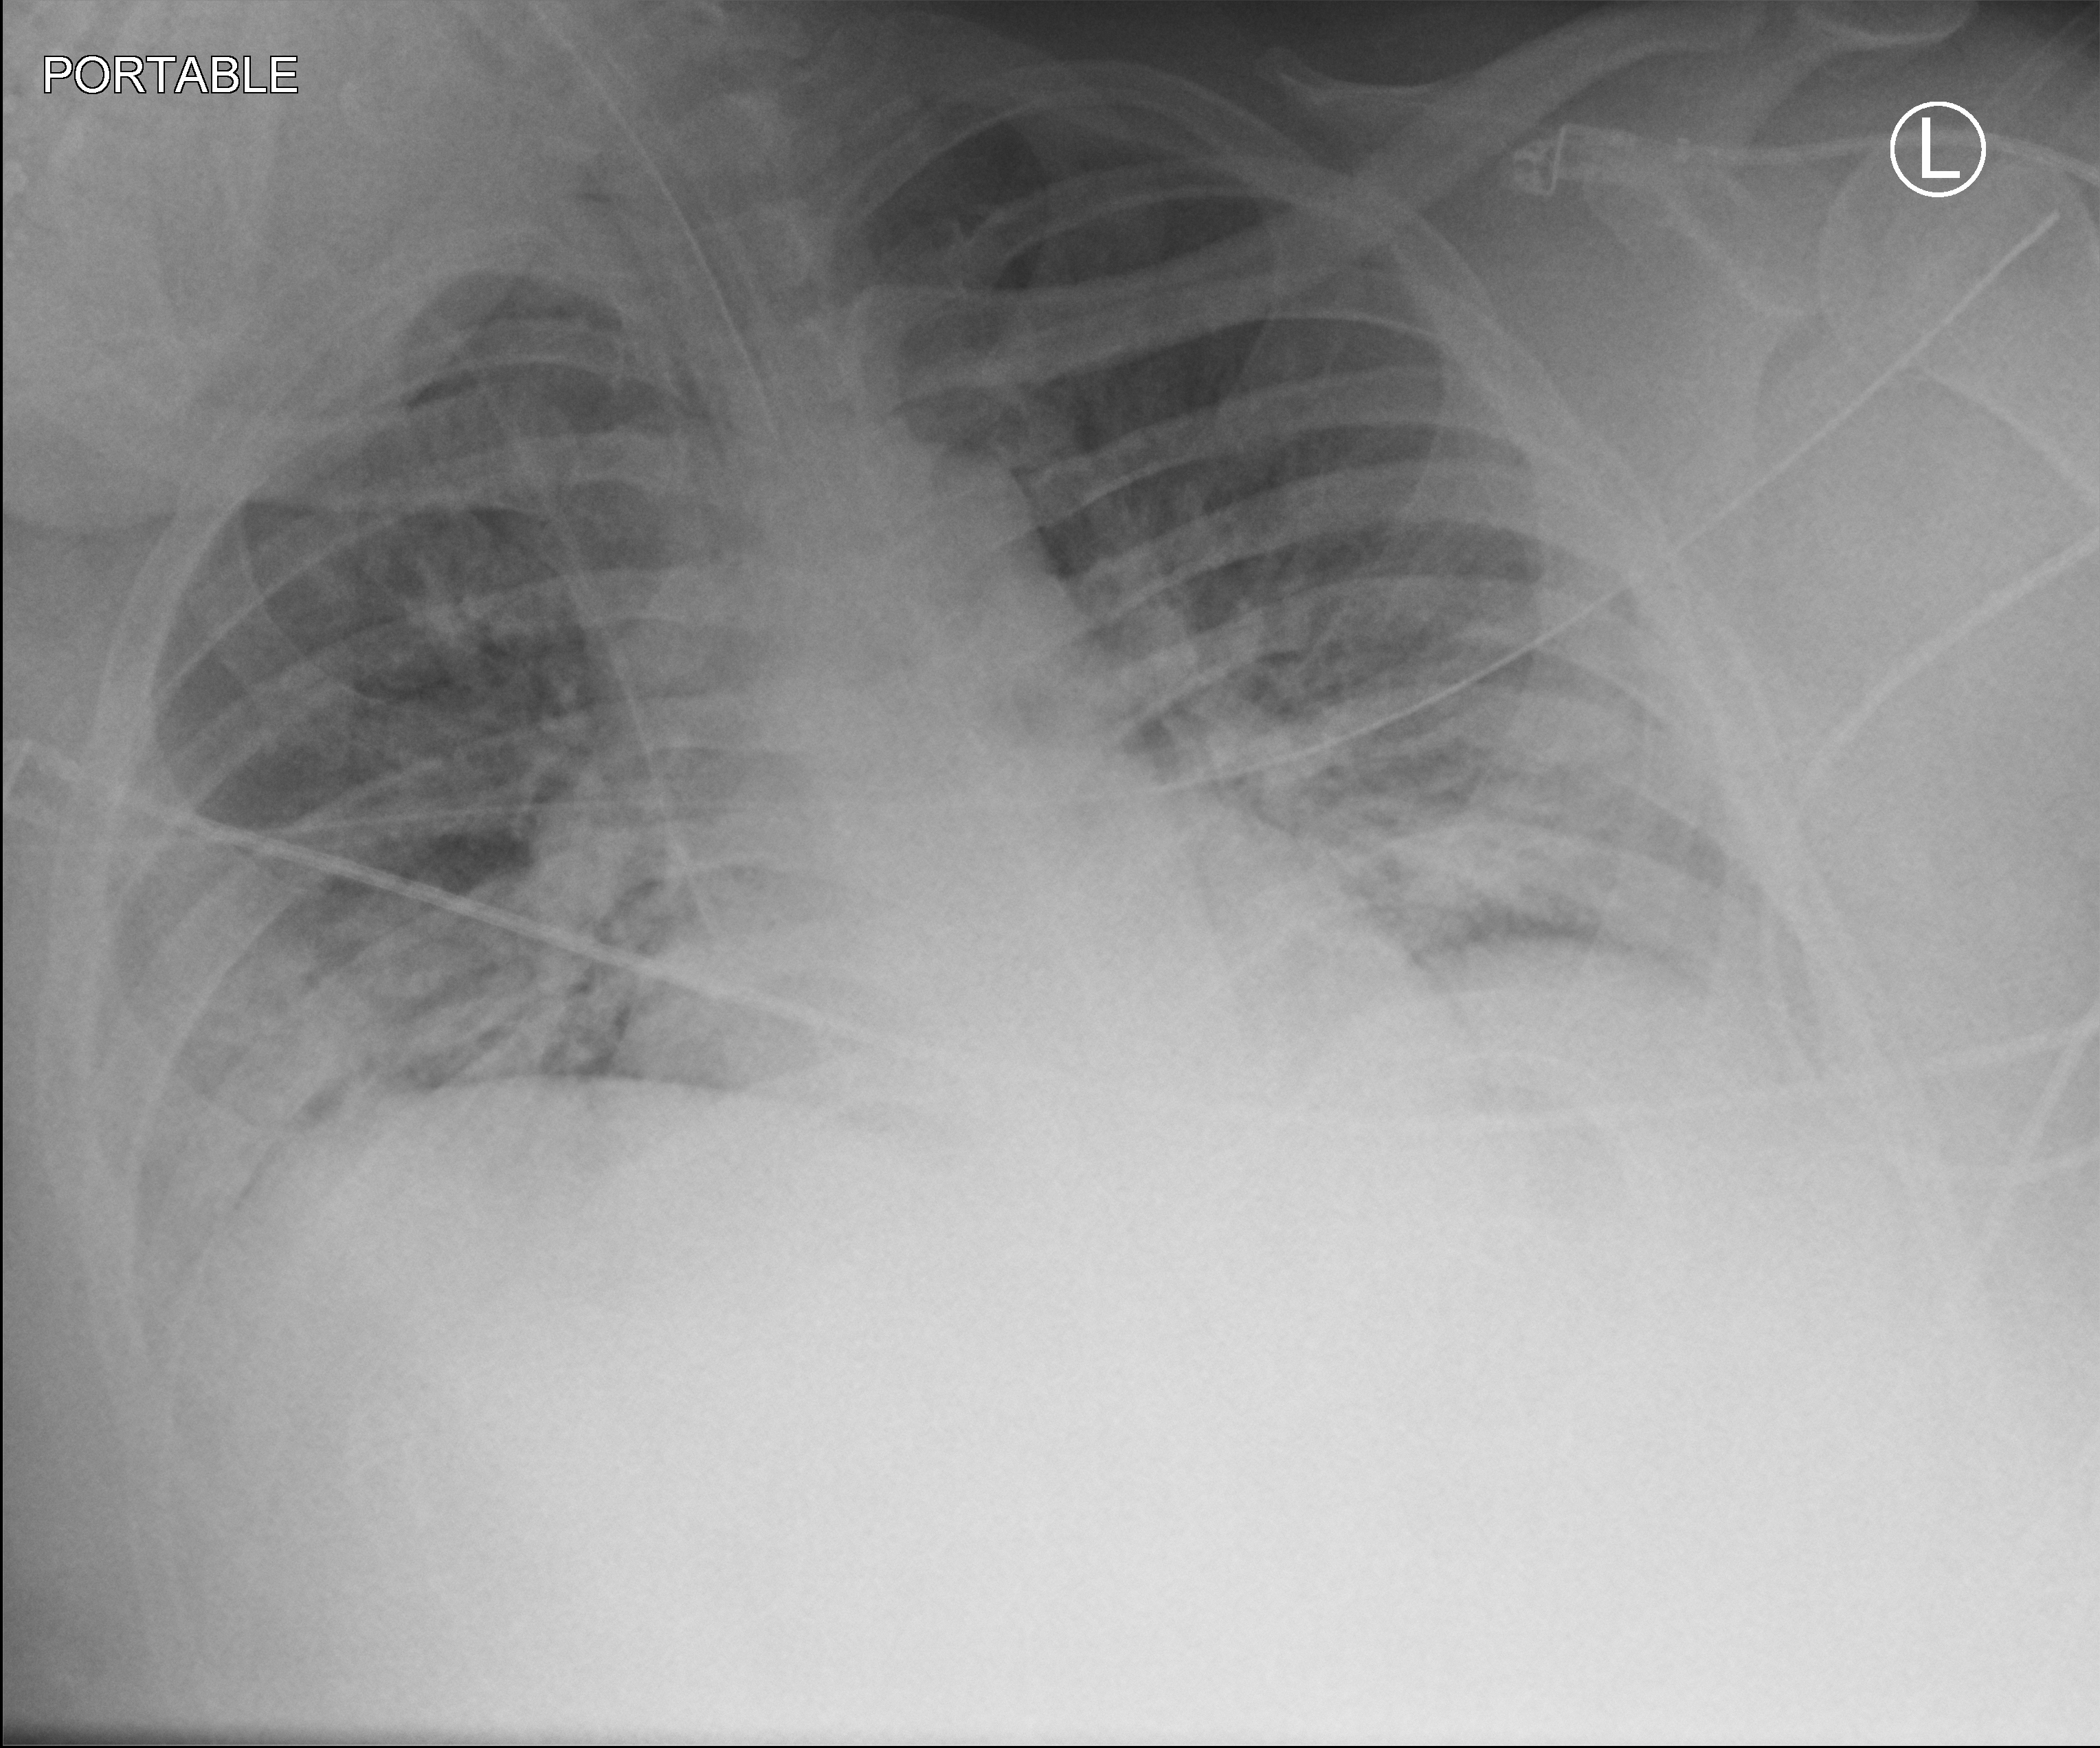
Bedside chest radiograph (computed radiography). Male patient hospitalised with COVID-19, age 18–59 years.
From the hospital-stay record, not from the radiograph (when in the stay this image was taken is not recorded): hypertension (admission record): no.